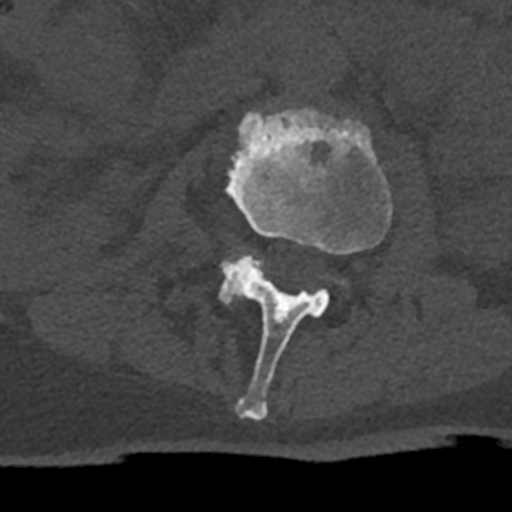
CT including the spine, one axial slice. Position 363 of 797 along the scan axis. Reconstruction kernel Br40s/3. 120 kVp. Bone window (W 1800 / L 400 HU). 512 × 512 image matrix, field of view 160 × 160 mm. Male patient, age 74 years. From the clinical record (not read from this slice): primary cancer: renal; vertebrae with lytic lesions (as recorded): T10, L1, L2, L3, L4, L5.
Annotated regions visible in this slice (semi-automatic segmentation, software-assisted and operator-edited):
- L2 vertebra: bounding box <225,108,392,420> (left, top, right, bottom; pixels)
- L3 vertebra: <219,250,264,305>